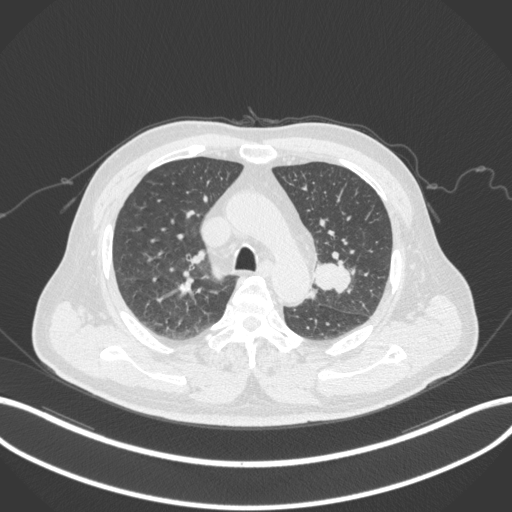
Chest CT, one axial slice; position 210 of 286 along the scan axis; reconstruction kernel B31f; lung window (W 1500 / L -600 HU); 512 × 512 image matrix, field of view 400 × 400 mm. Patient: male, 67 years. Case-level facts recorded for this patient, not image findings: clinical TNM (as recorded): T2a N1 M0.
Outlined on this slice (rectangle marked by the reading radiologist):
- lung tumour (recorded histology: adenocarcinoma): bounding box (x1, y1, x2, y2) in pixels: (314, 257, 355, 295)